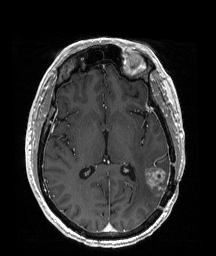
Brain MRI from a brain-tumour surgery series, one axial slice; position 94 of 192 along the scan axis; T1-weighted post-contrast; 1 mm slice thickness; 216 × 256 image matrix. From the clinical record (not read from this slice): histopathology: Glioblastoma; WHO grade: 4; IDH mutation: no.
Annotated regions visible in this slice (outlined manually by an expert reader):
- tumour: bounding box [x1, y1, x2, y2] px = [144, 166, 170, 187]